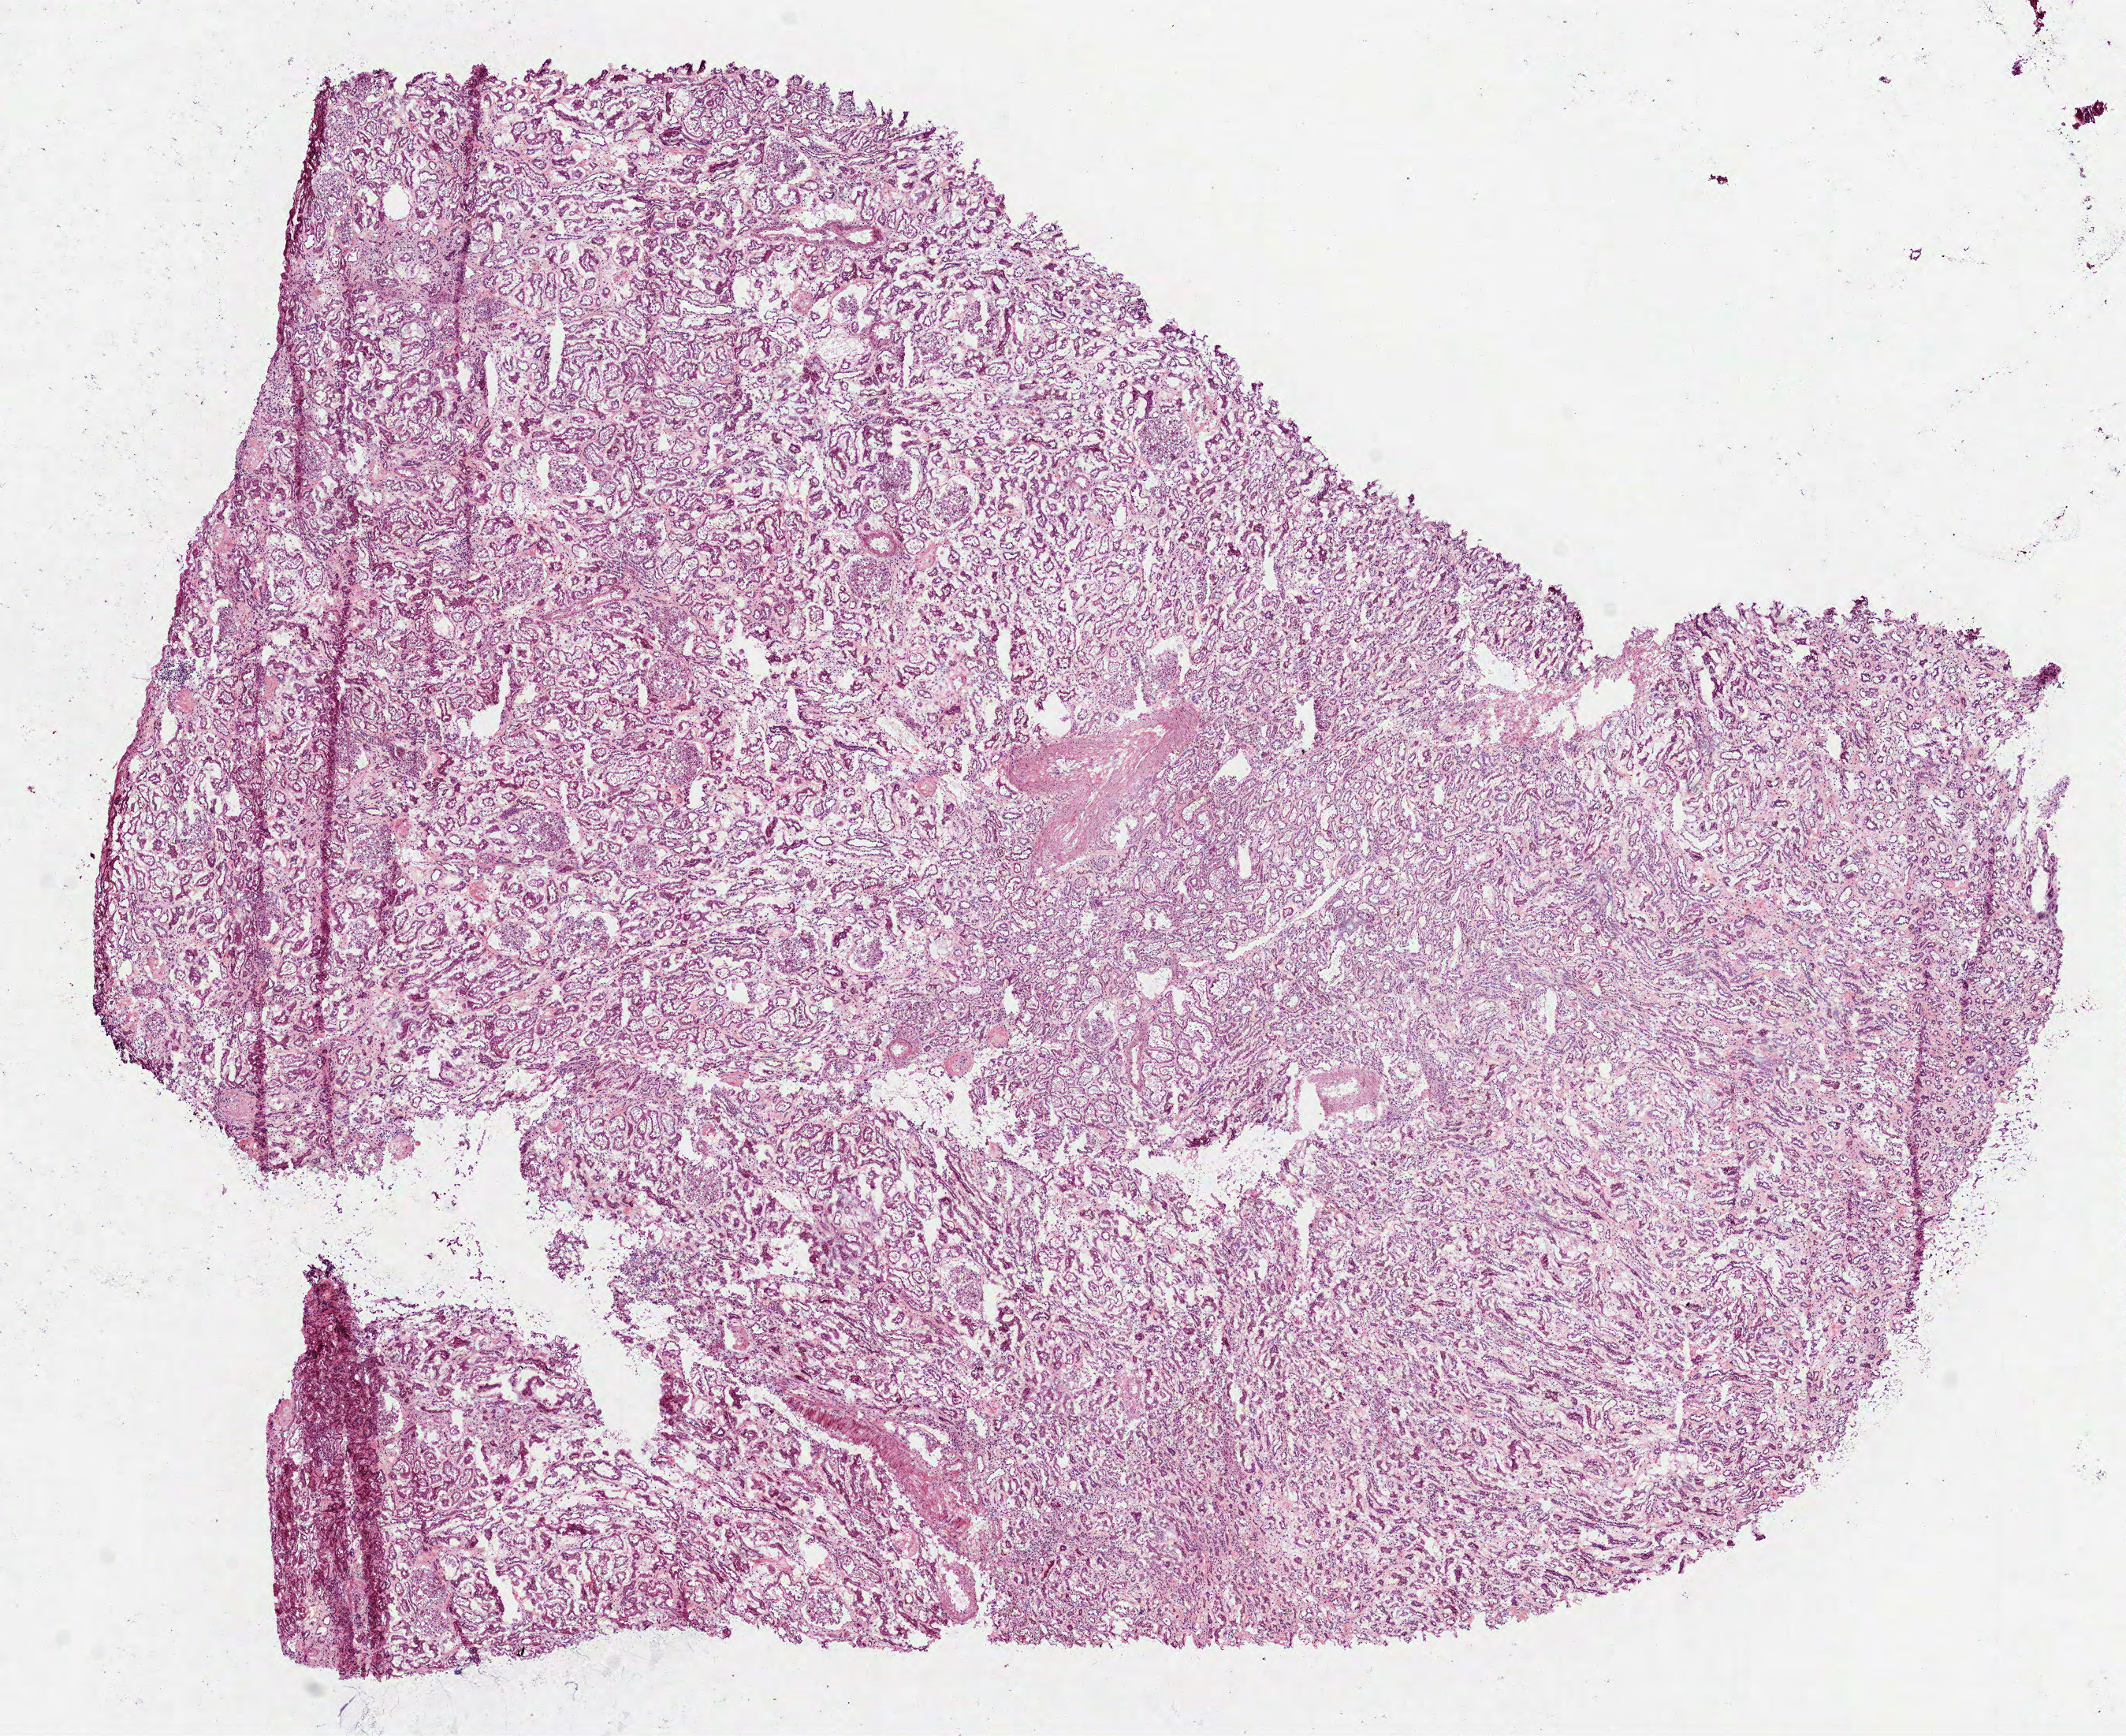
H&E-stained whole-slide image, whole scanned area (about 10.9 x 8.9 mm) shown as a low-resolution overview; frozen section from the top of the tissue portion; sample: solid tissue normal (non-tumour tissue), kidney. Patient: female, age at initial diagnosis 71 years.
This section: solid tissue normal (non-tumour) sample from the same patient. Patient diagnosis: Papillary adenocarcinoma, NOS.